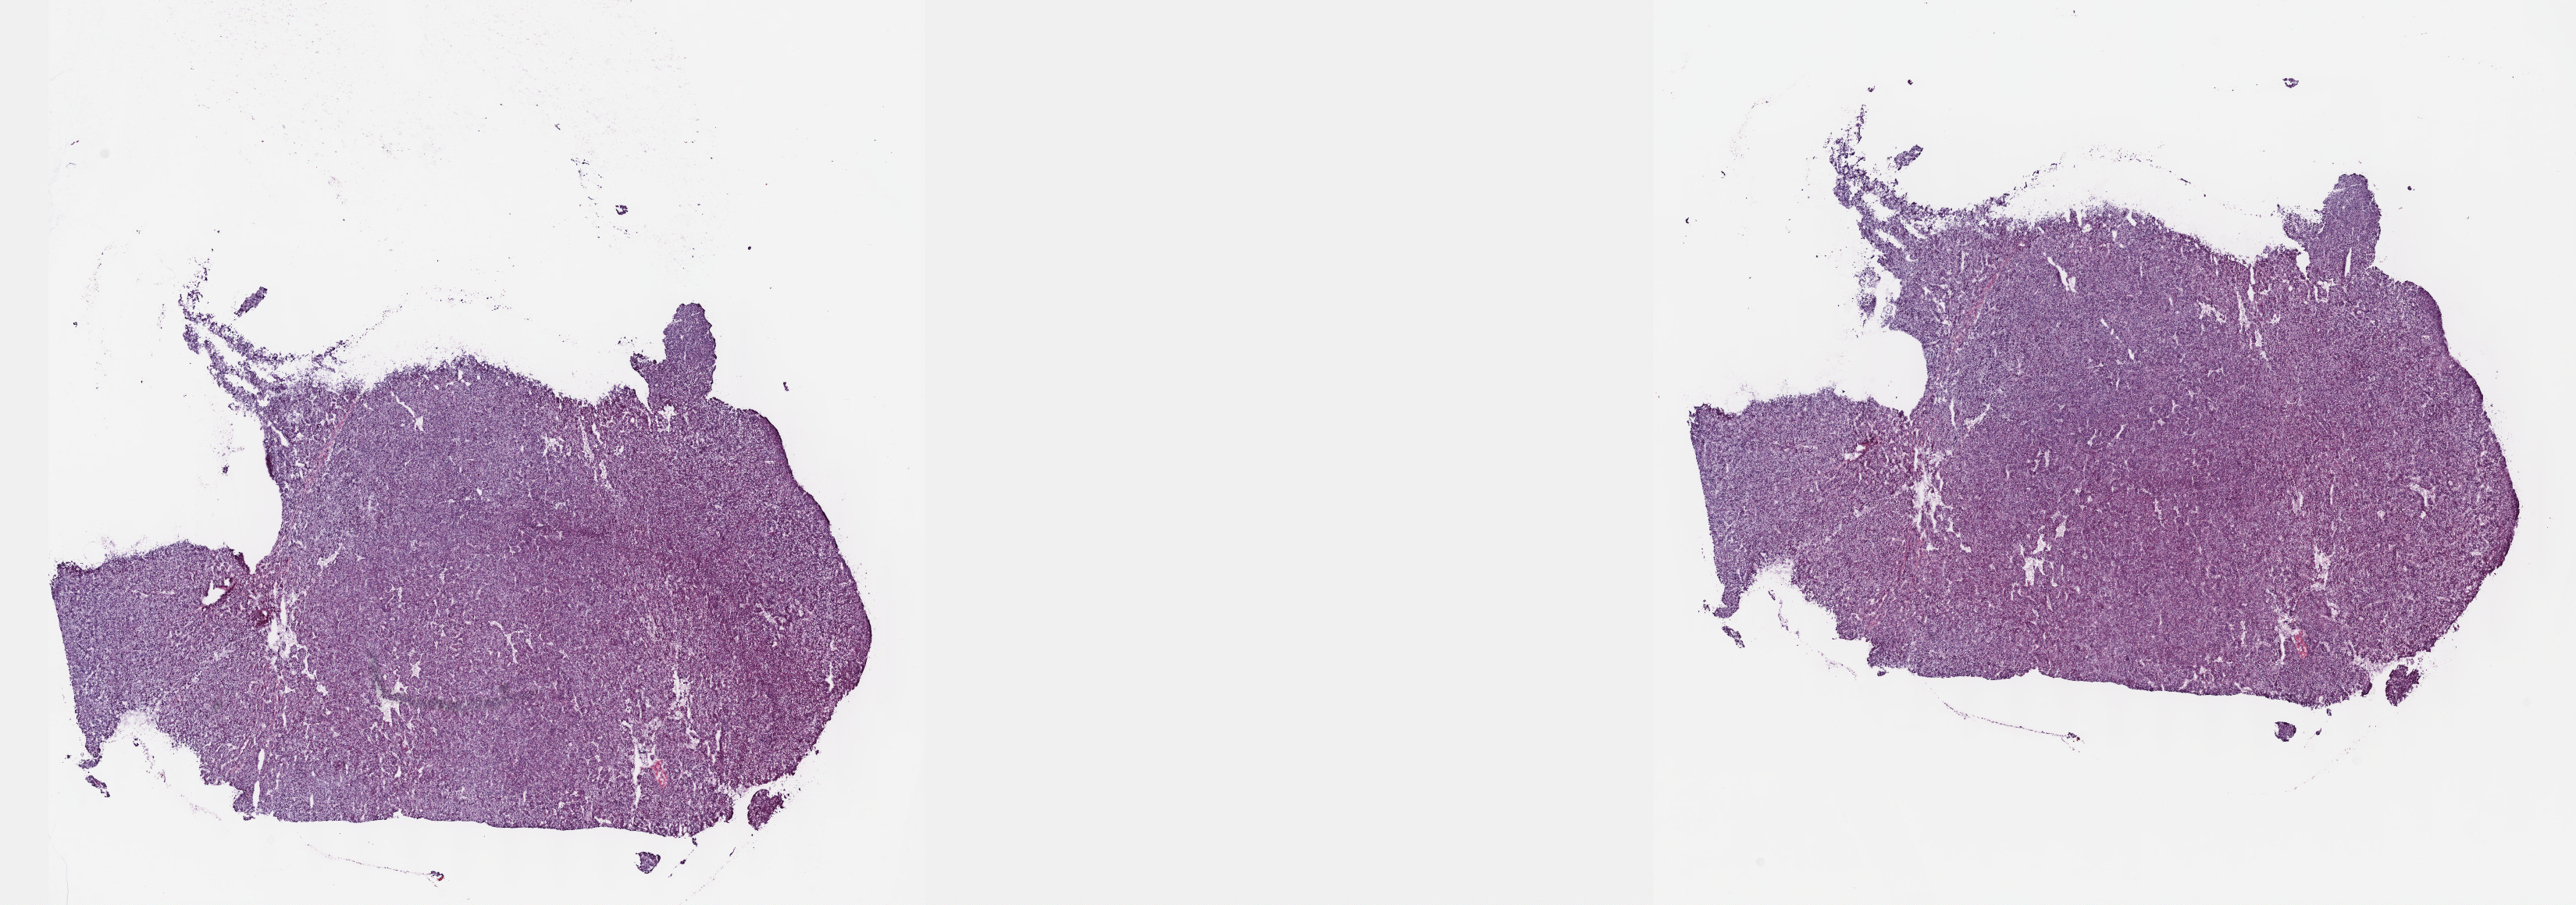
Whole-slide histology image, H&E — low-resolution overview of the scanned area, about 26.7 x 9.4 mm (acquisition: 40x scan). Frozen section from the top of the tissue portion. Sample: primary tumour, liver. Patient: male, age at initial diagnosis 59 years.
Pathologic diagnosis: Hepatocellular carcinoma, NOS.